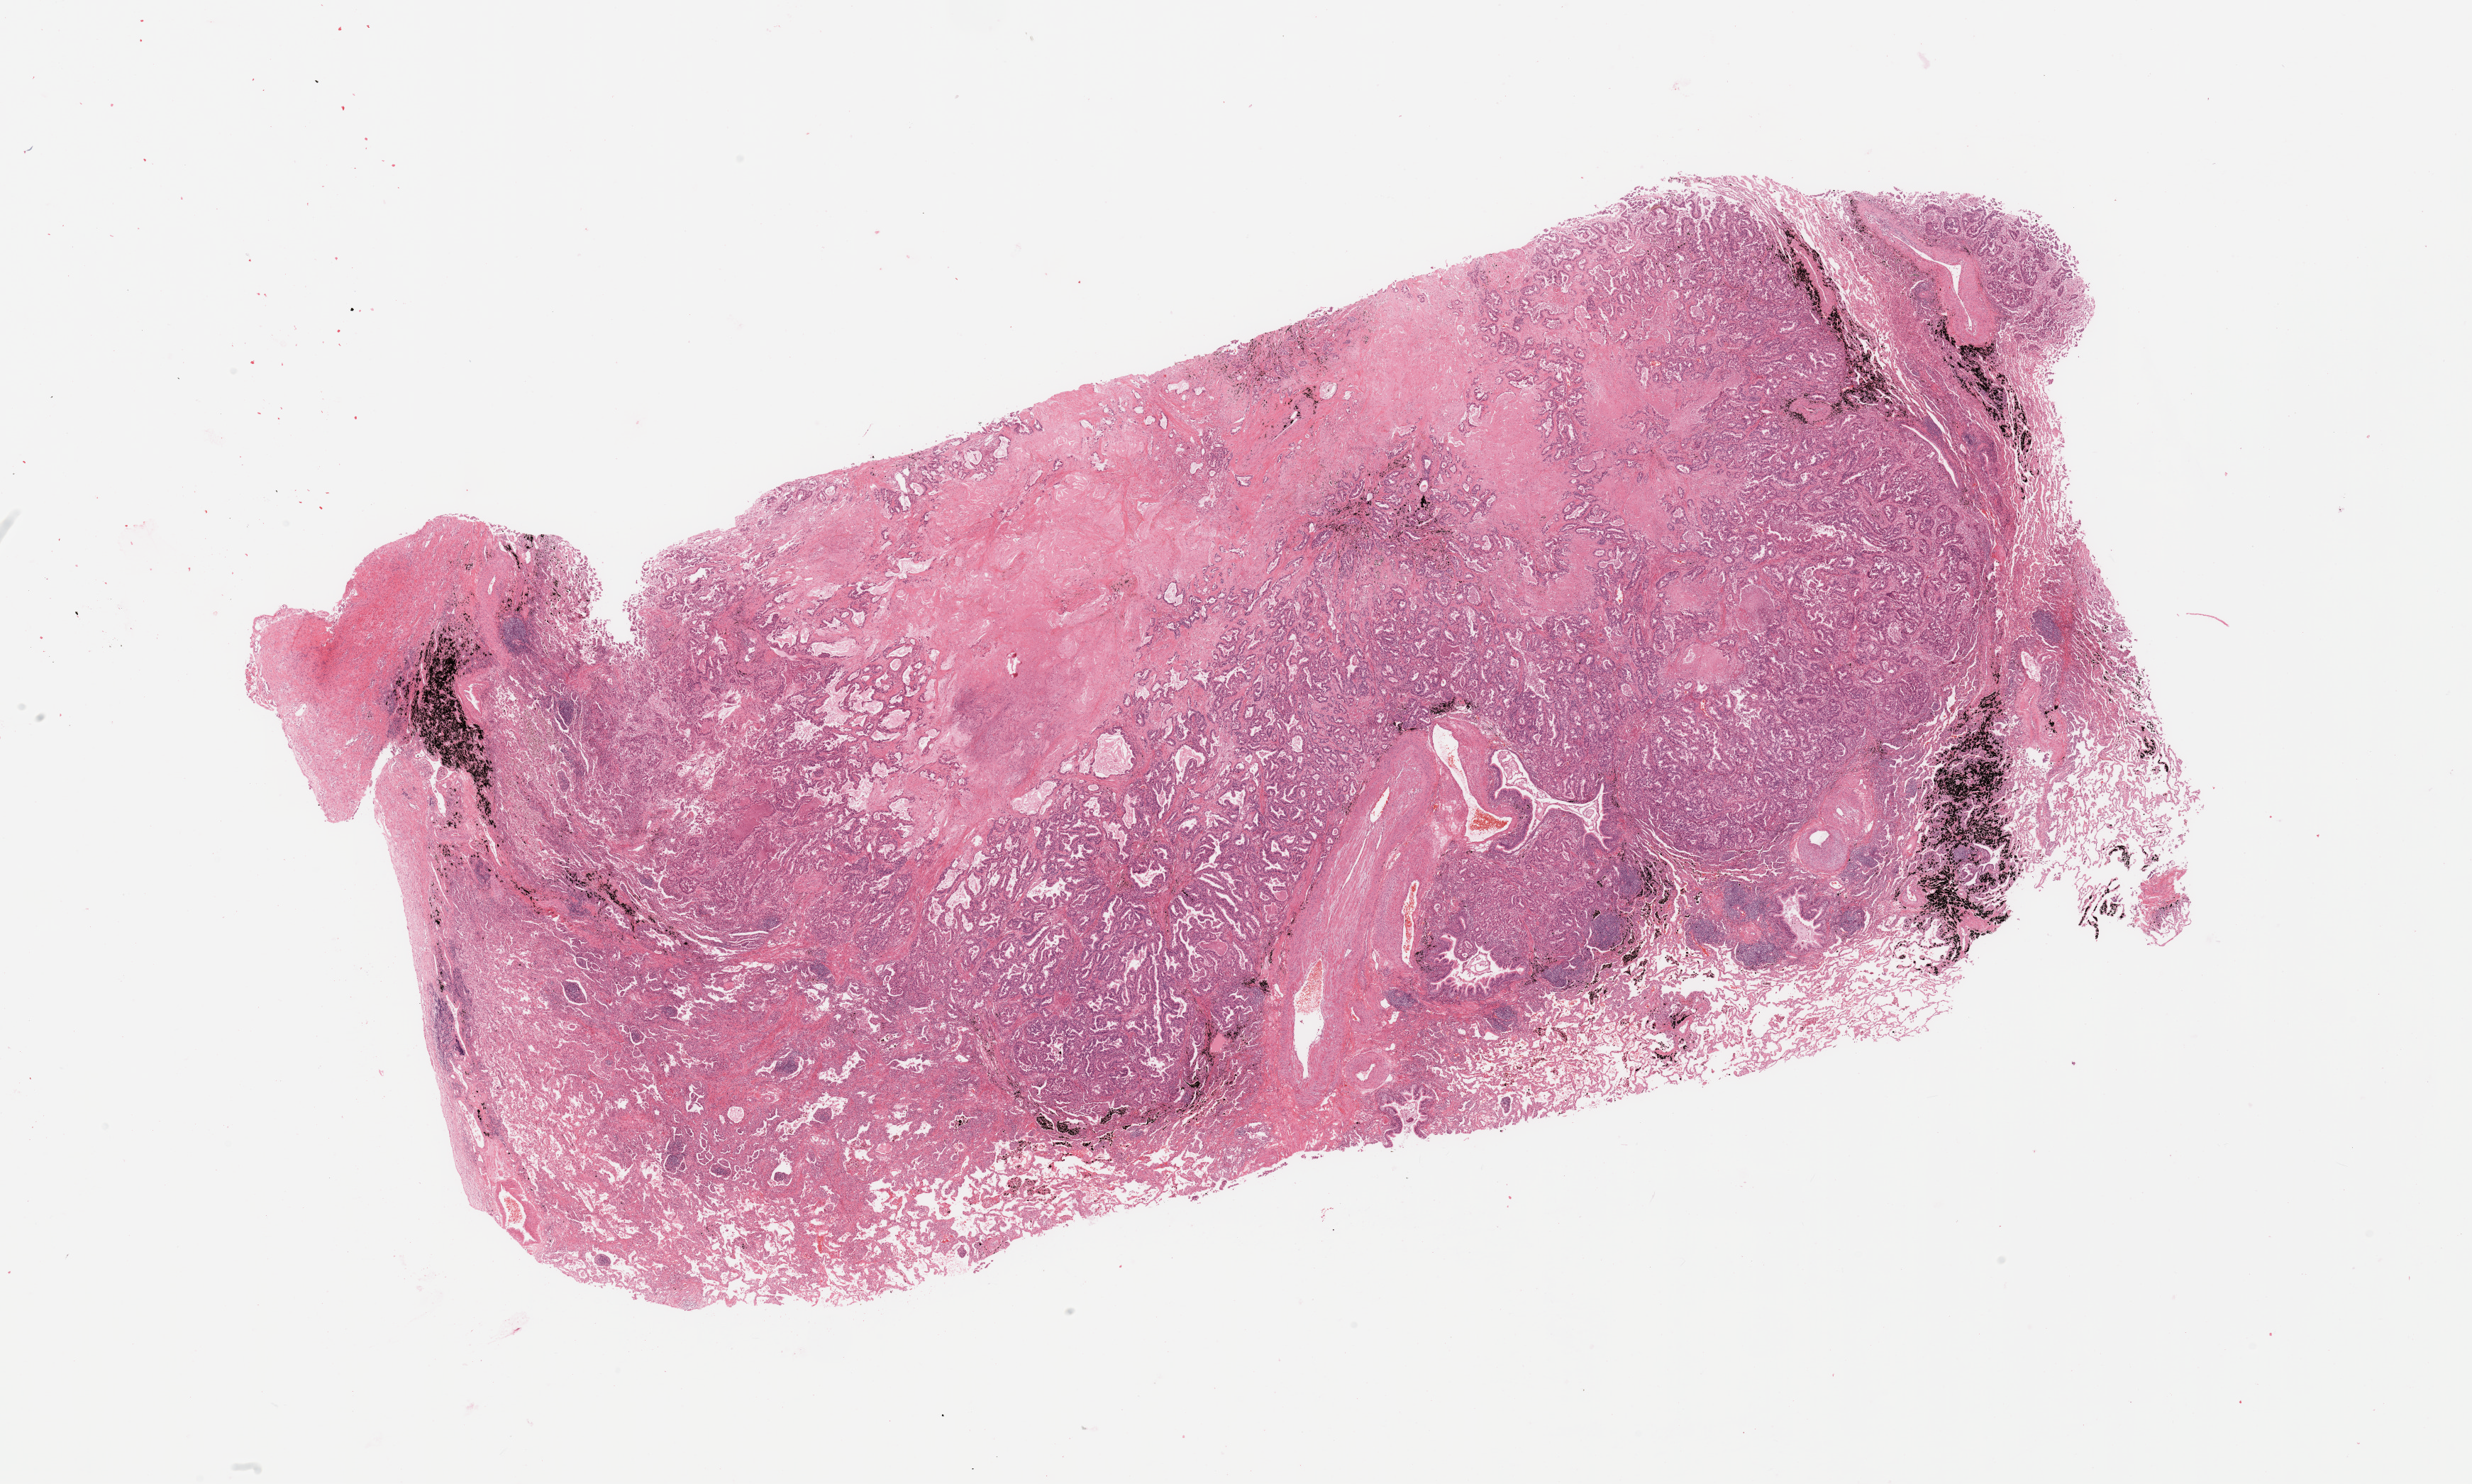
Digitized H&E tissue section (whole slide), whole scanned area (about 27.6 x 16.5 mm, acquisition: 20x scan) shown as a low-resolution overview, lung, tumour tissue. 59-year-old male patient. Histologic grade: G2 (moderately differentiated).
- primary tumour site (as recorded): left upper lobe
- diagnosis: Adenocarcinoma, NOS
- AJCC pathologic stage: IB